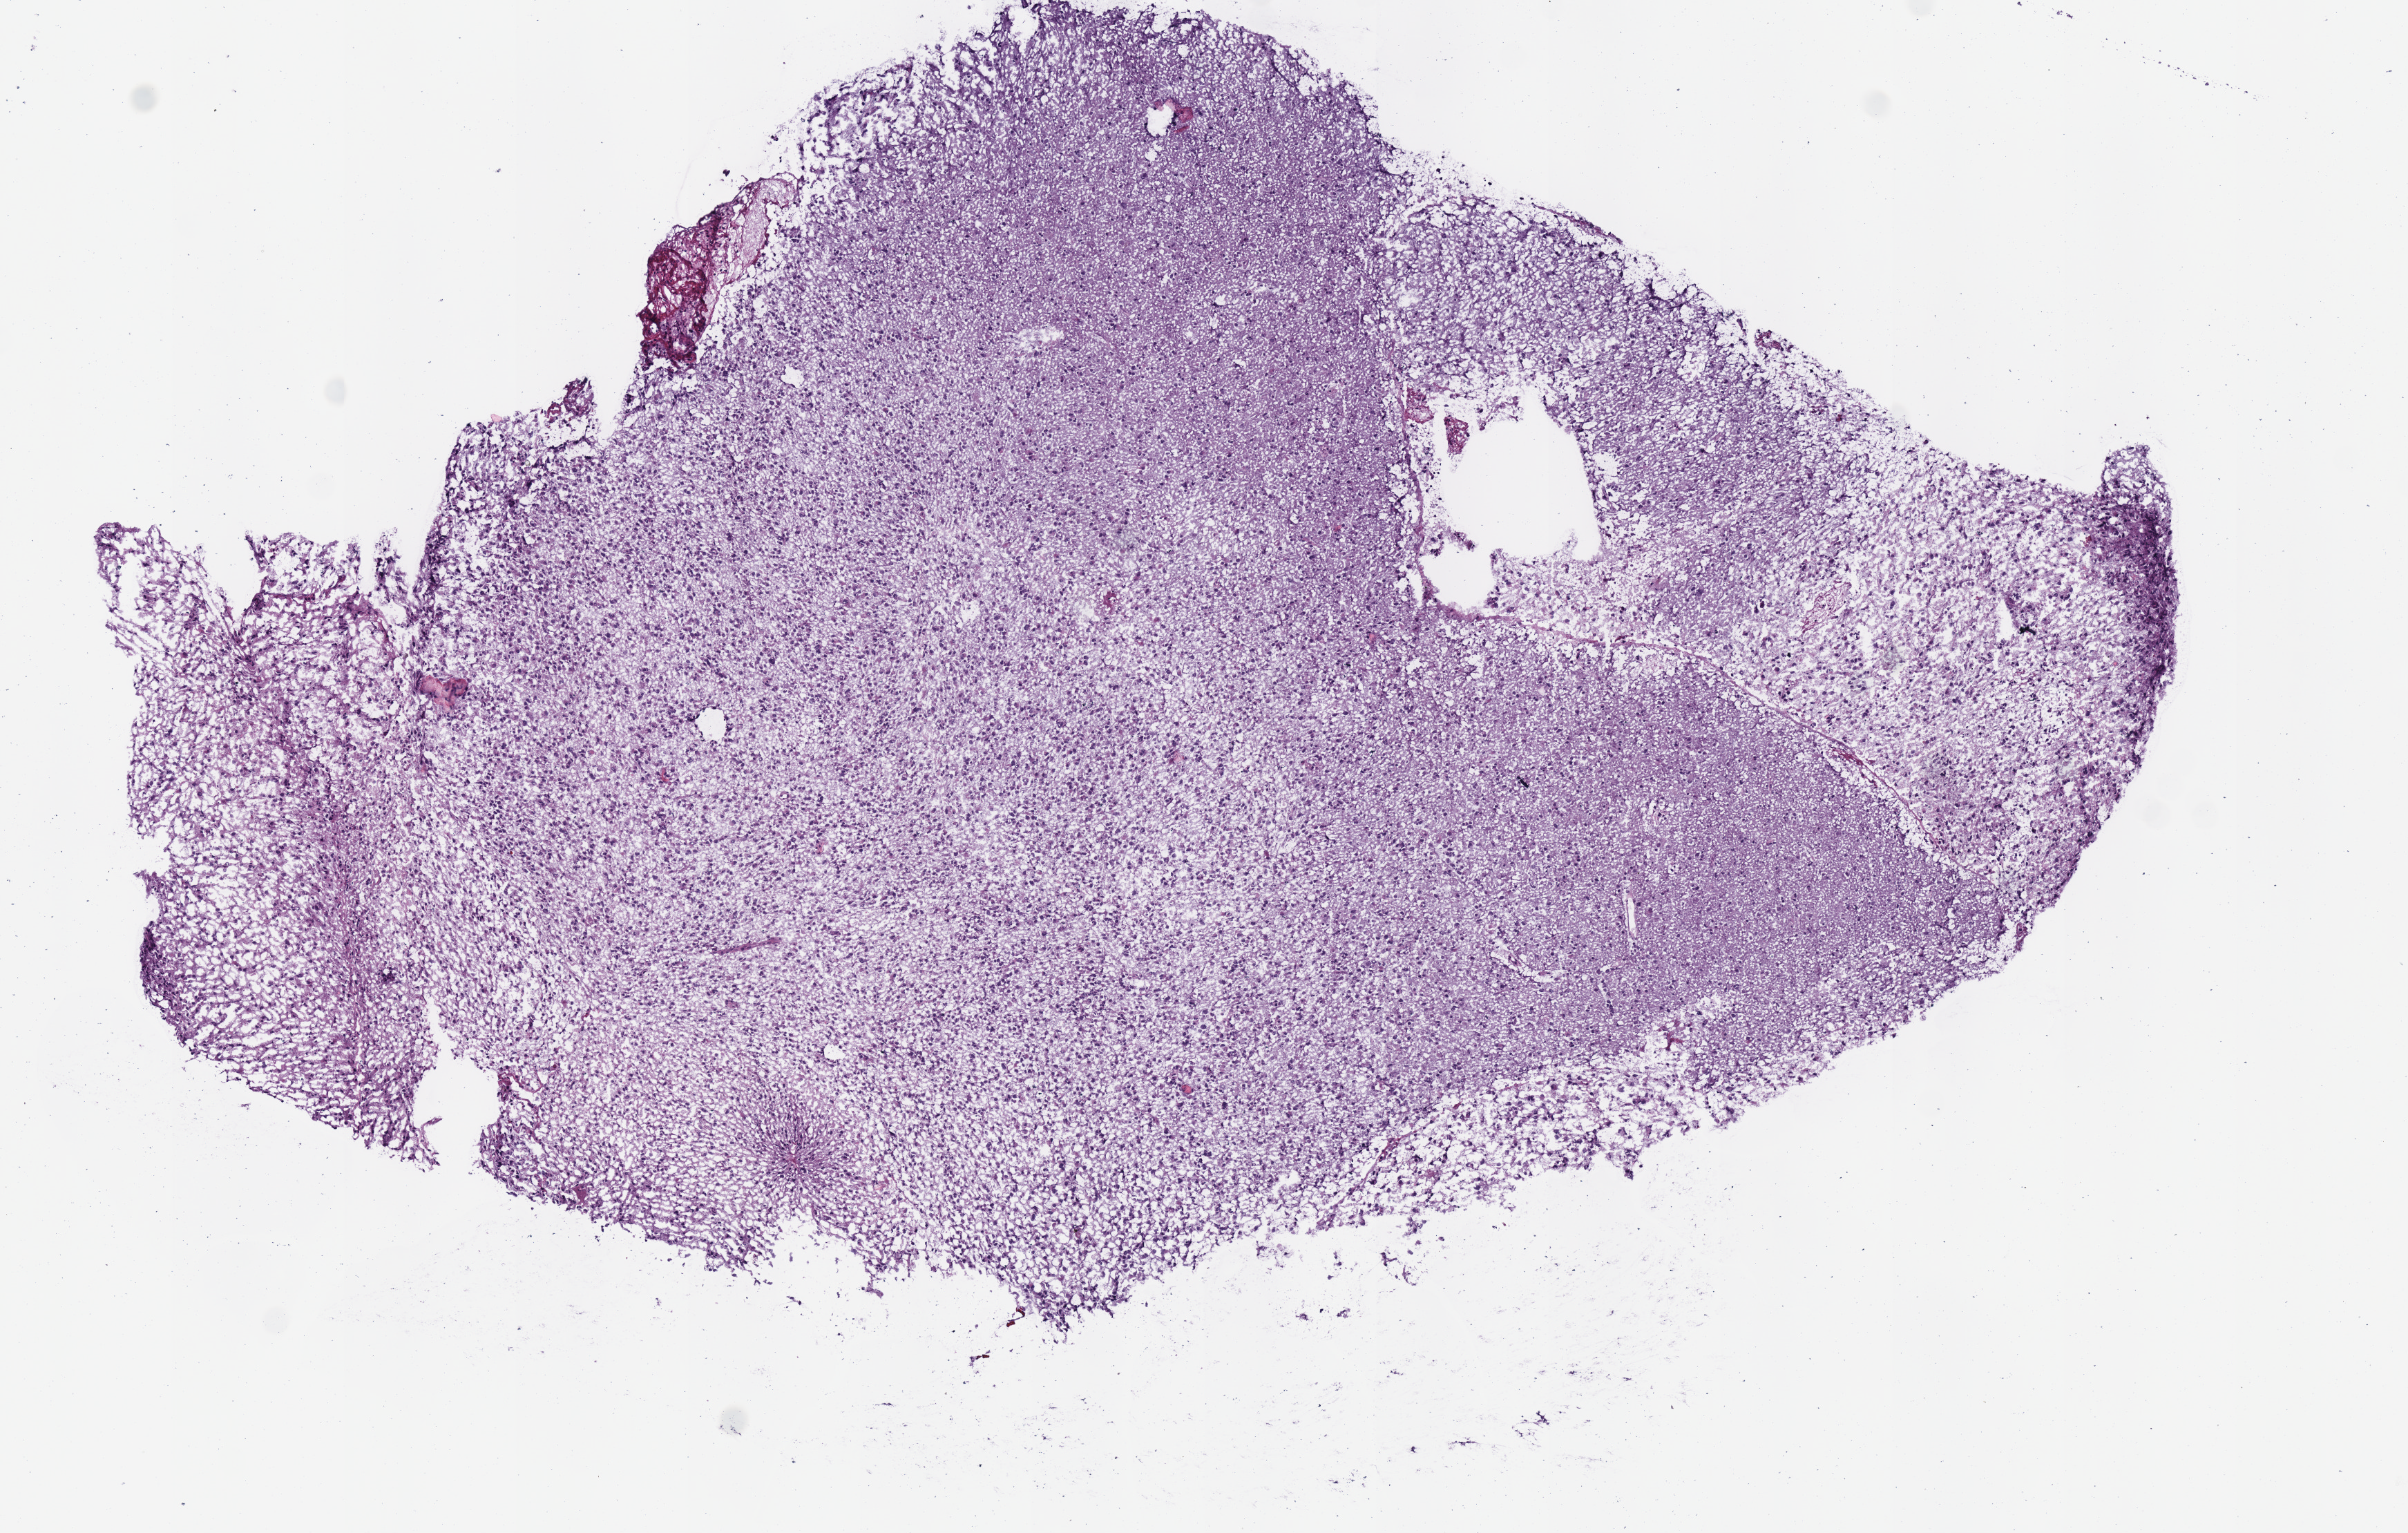
Hematoxylin and eosin (H&E) stained whole-slide image — shown as a low-resolution overview of the whole scanned area (about 6.9 x 4.4 mm). Frozen section. Primary tumour sample from the brain. Female patient; age at initial diagnosis 26 years. Histologic grade: G2 (moderately differentiated). Pathologist review of this section (percent, as recorded): tumour cells 100%, tumour nuclei 75%, normal cells 0%, stromal cells 0%, necrosis 0%.
- histologic diagnosis: Oligodendroglioma, NOS (cerebrum)